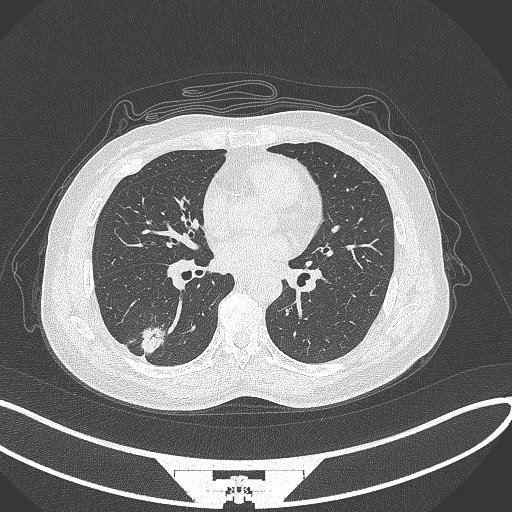
Chest CT, one axial slice. Slice 137 of 352 in the series (ordered by position). Lung window (W 1500 / L -600 HU). 1 mm slice thickness. 512 × 512 image matrix, field of view 400 × 400 mm. Patient: female, 55 years. Case-level facts recorded for this patient, not image findings: clinical TNM (as recorded): T1c N1 M0.
Outlined on this slice (rectangle marked by the reading radiologist):
- lung tumour (recorded histology: adenocarcinoma): bounding box (x1, y1, x2, y2) in pixels: (138, 325, 169, 357)